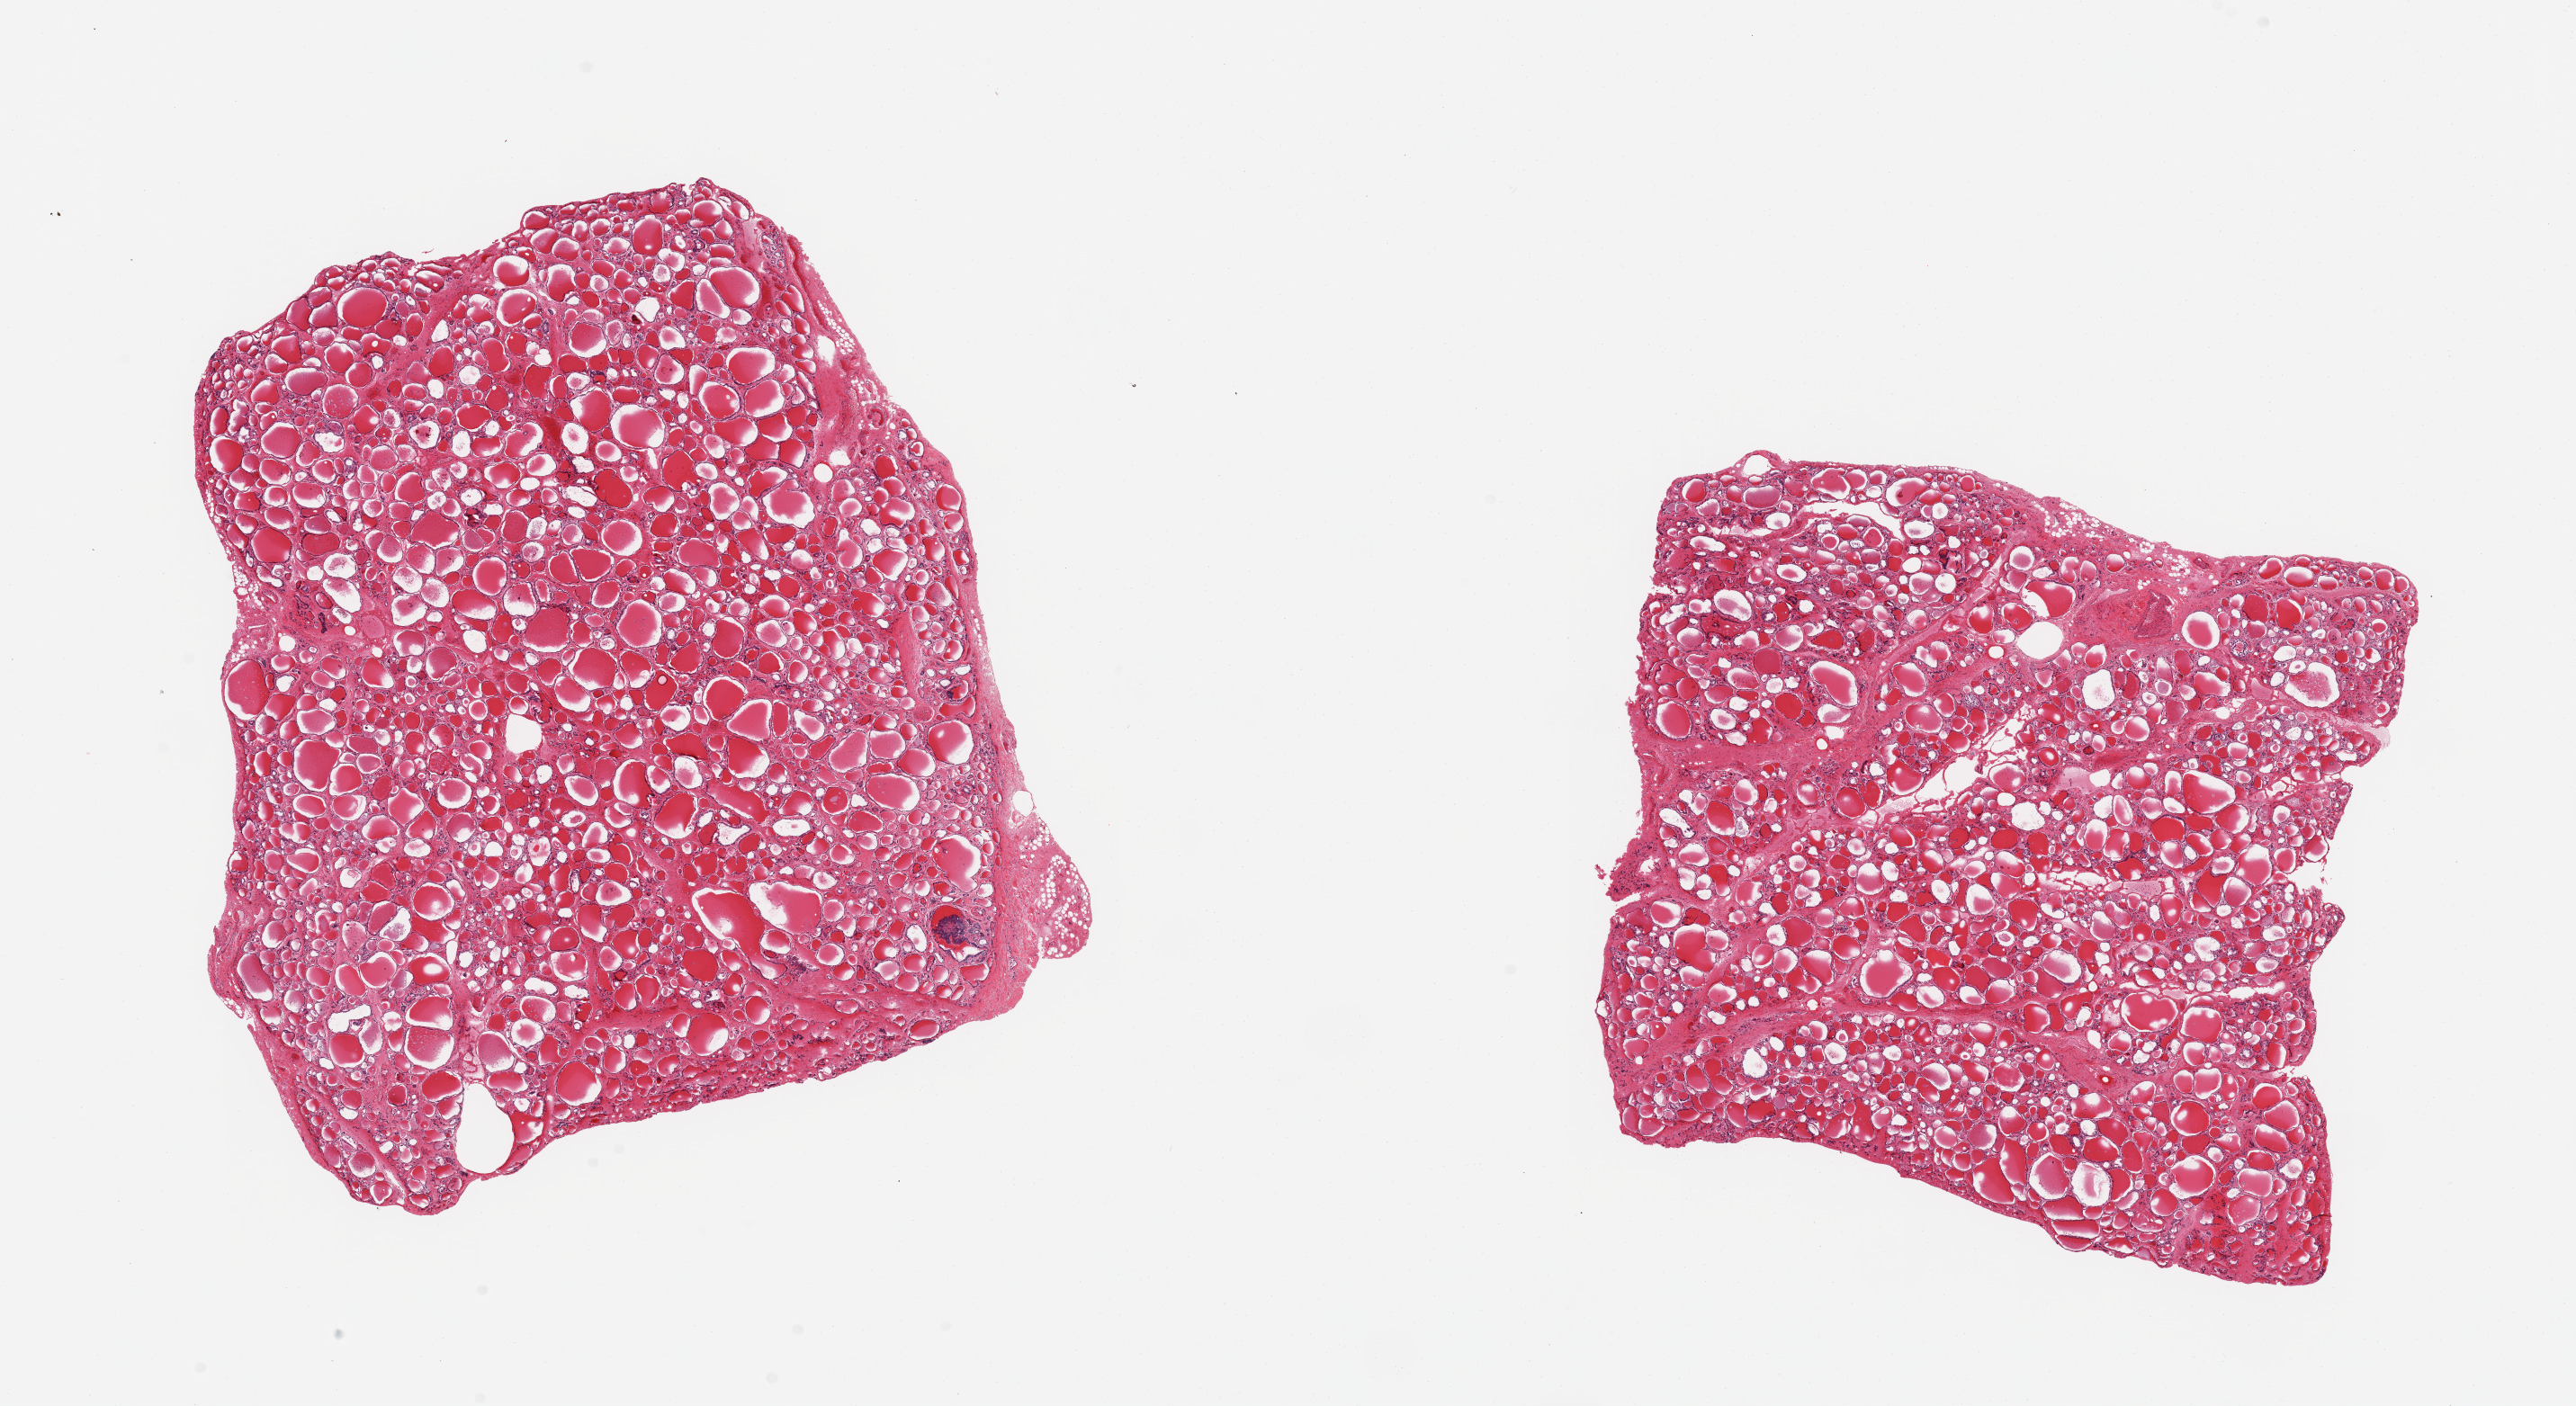
Whole-slide image, haematoxylin and eosin stain, shown as a low-resolution overview of the whole scanned area (about 22.6 x 12.4 mm, slide scanned at 20x). PAXgene-fixed paraffin-embedded (PFPE) section. Section of thyroid (target tissue). Donor tissue sample. Male donor.
Reviewer comment on this tissue sample: 2 pieces, no abnormalities.